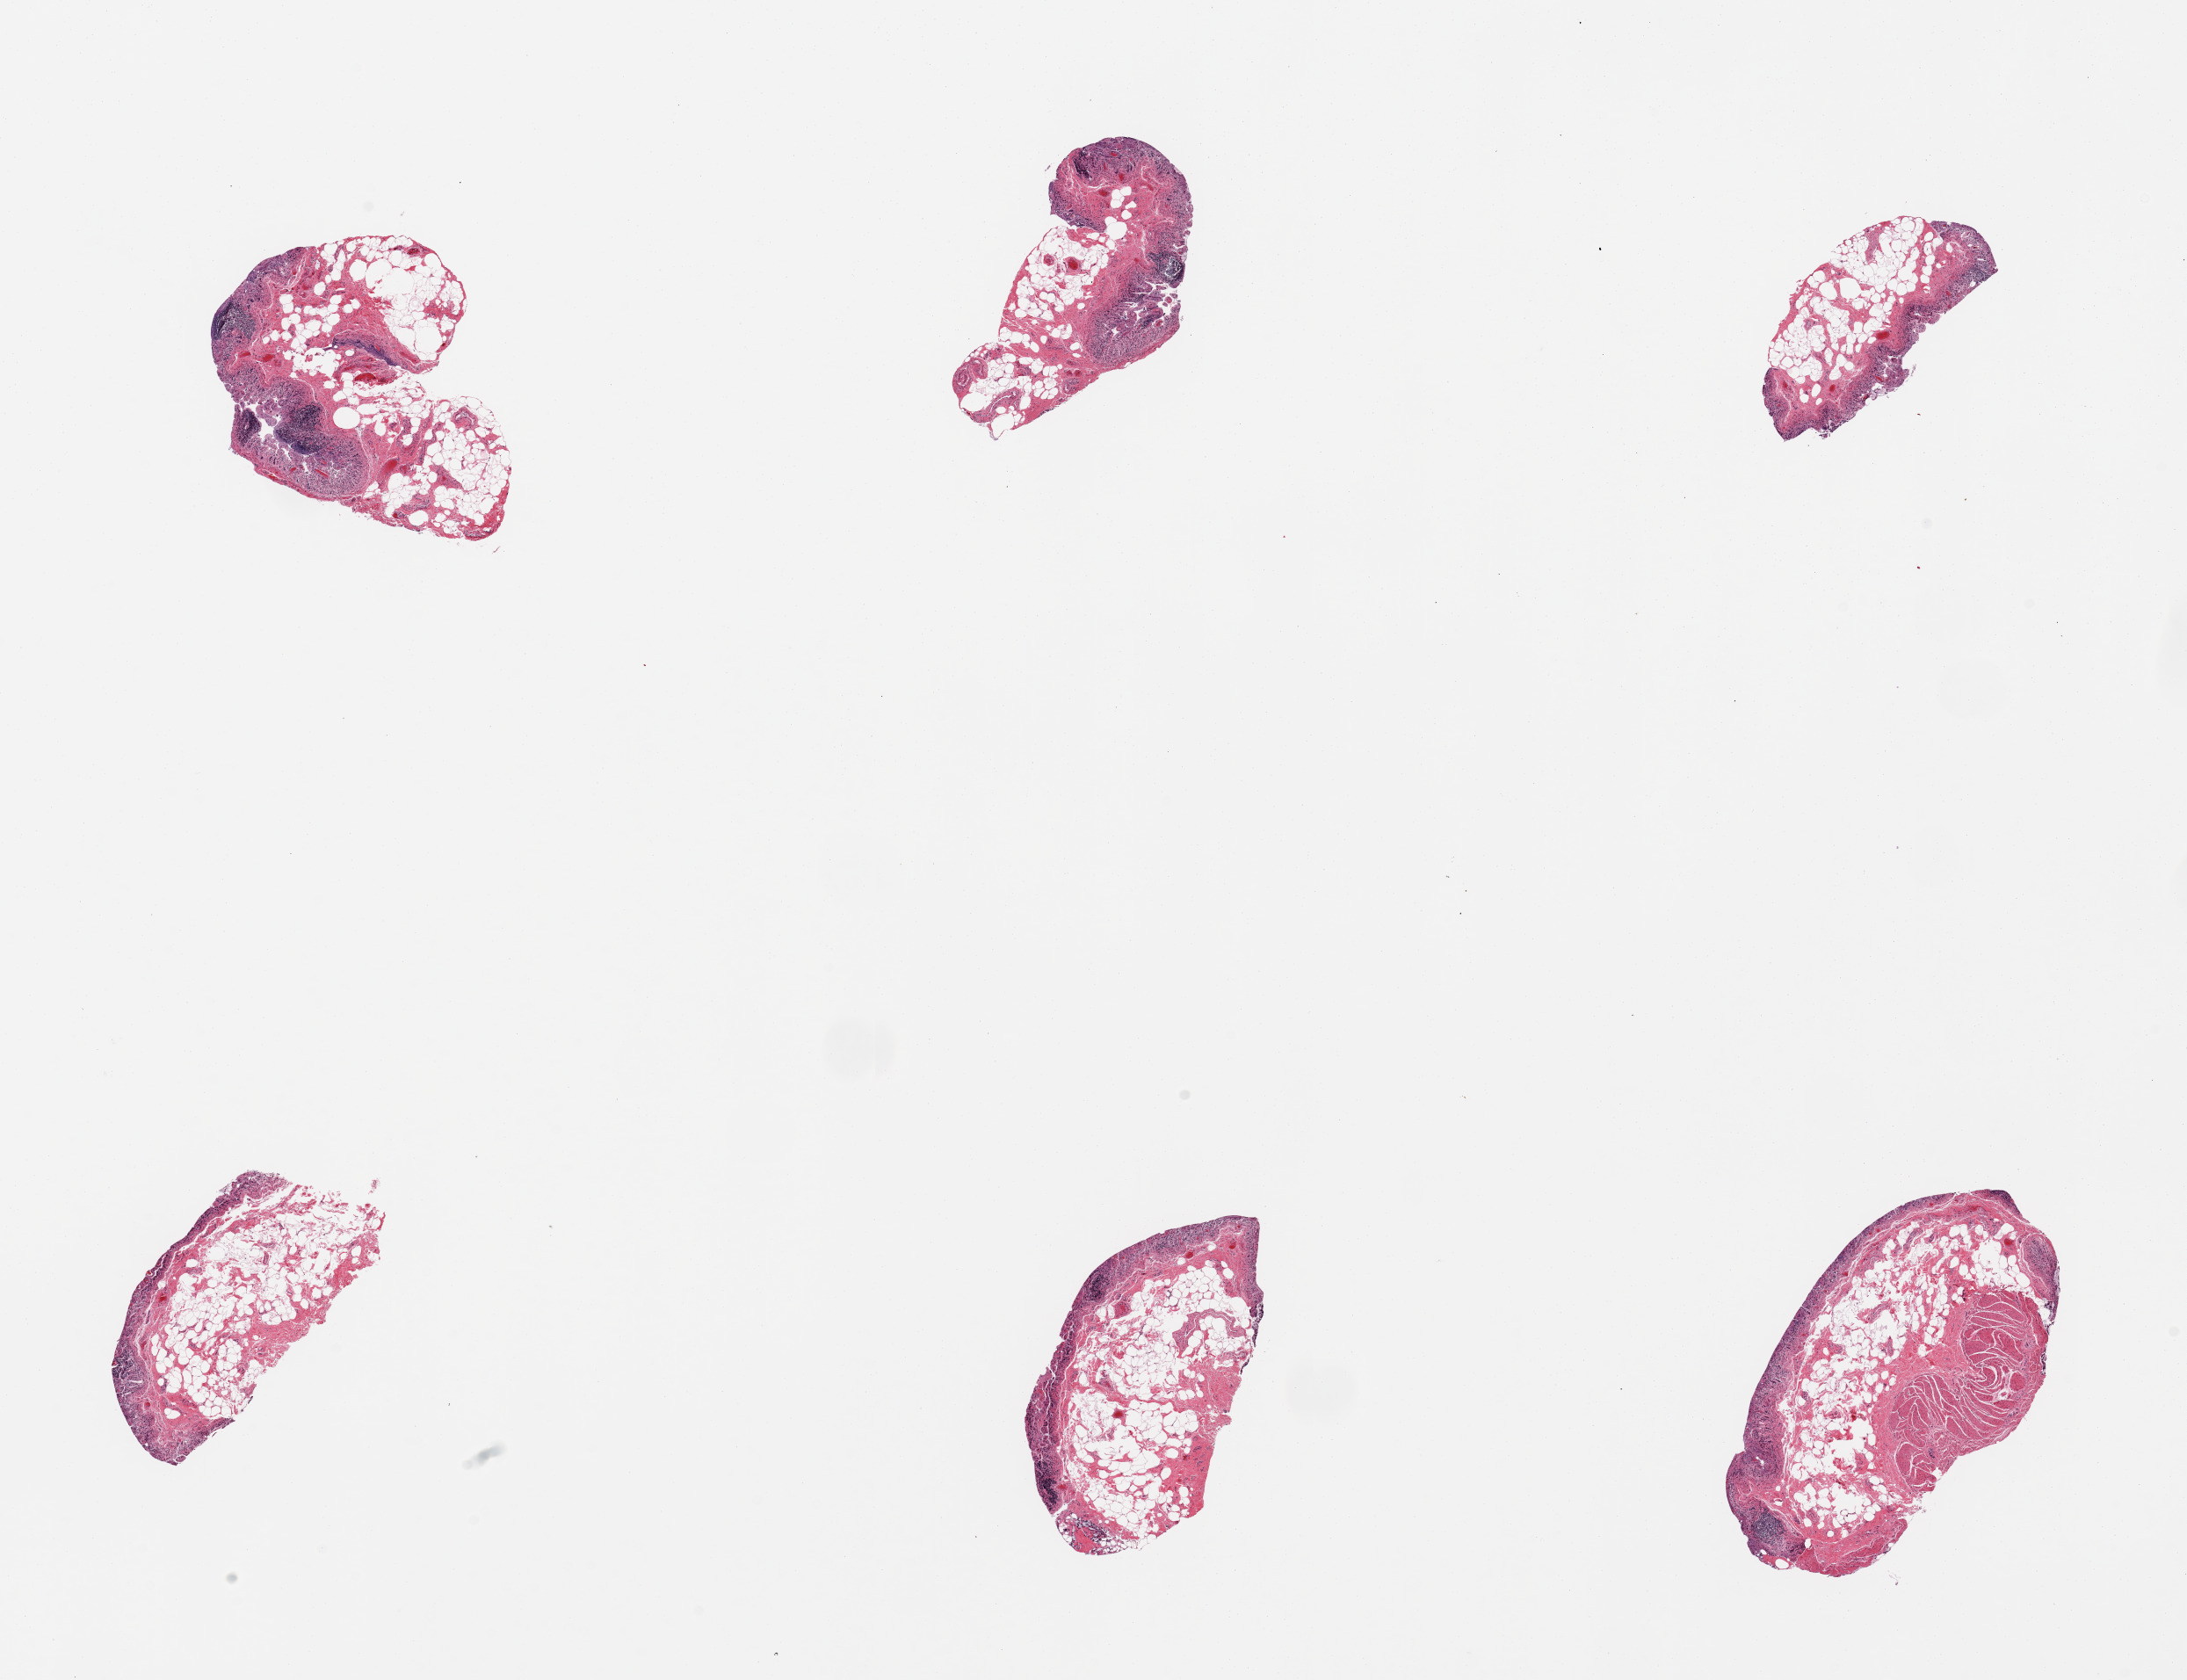
Hematoxylin and eosin (H&E) whole-slide image, brightfield — a low-resolution overview of the entire scanned area, about 19.7 x 15.1 mm. Male donor.
* specimen: PAXgene-fixed paraffin-embedded (PFPE) section; section of ileum (target tissue); tissue donor sample